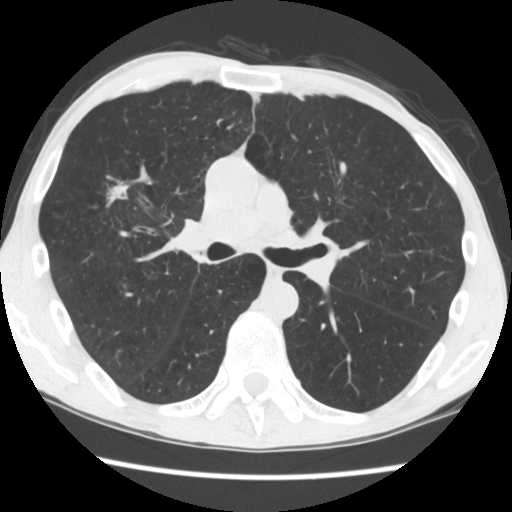
Low-dose screening chest CT, one axial slice; position 104 of 181 along the scan axis; reconstruction kernel STANDARD; 120 kVp; lung window (W 1500 / L -600 HU); 512 × 512 image matrix, field of view 330 × 330 mm.
Outlined on this slice (manually delineated by an expert):
- lesion 1 (tumor, upper lobe of right lung): bounding box <106,184,129,207> (left, top, right, bottom; pixels)